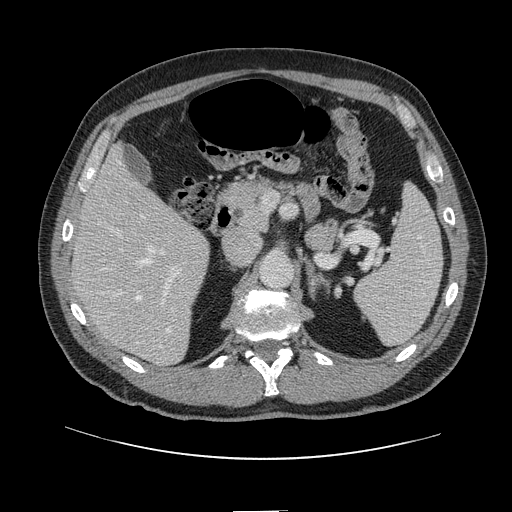
Contrast-enhanced abdominal CT, one axial slice. Position 70 of 161 along the scan axis. Intravenous contrast given. Soft-tissue window (W 400 / L 40 HU). 2.5 mm slice thickness. 512 × 512 image matrix. Male patient, age 66 years. Case-level facts recorded for this patient, not image findings: diagnosis: colorectal cancer liver metastases, imaged before liver resection; multiple liver metastases: no.
Annotated regions visible in this slice (expert manual segmentation):
- hepatic veins: bounding box [x1, y1, x2, y2] px = [137, 247, 174, 333]
- liver: [75, 150, 209, 364]
- planned liver remnant (the part of the liver to remain after resection): [75, 150, 186, 291]
- portal vein (with intrahepatic branches): [118, 213, 183, 307]